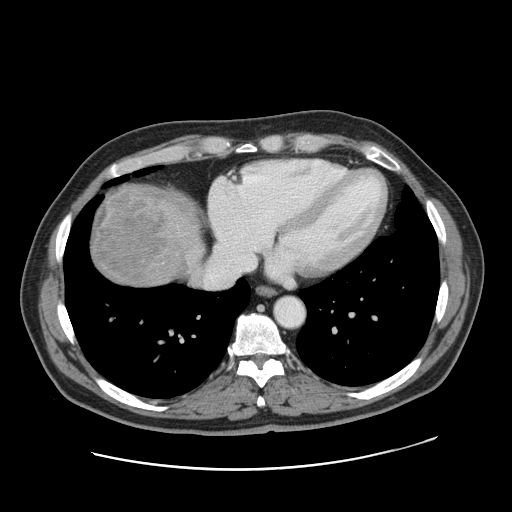
Contrast-enhanced abdominal CT, one axial slice. Position 154 of 178 along the scan axis. Soft-tissue window (W 400 / L 40 HU). 512 × 512 image matrix, field of view 403 × 403 mm. Male patient, age 63 years. Case-level facts recorded for this patient, not image findings: diagnosis: colorectal cancer liver metastases, imaged before liver resection; multiple liver metastases: yes; largest metastasis: 8 cm; chemotherapy before resection: no.
Structures marked on this image (outlined manually by an expert reader):
- liver: bounding box [x1, y1, x2, y2] px = [89, 183, 202, 289]
- liver metastasis: [94, 186, 164, 282]